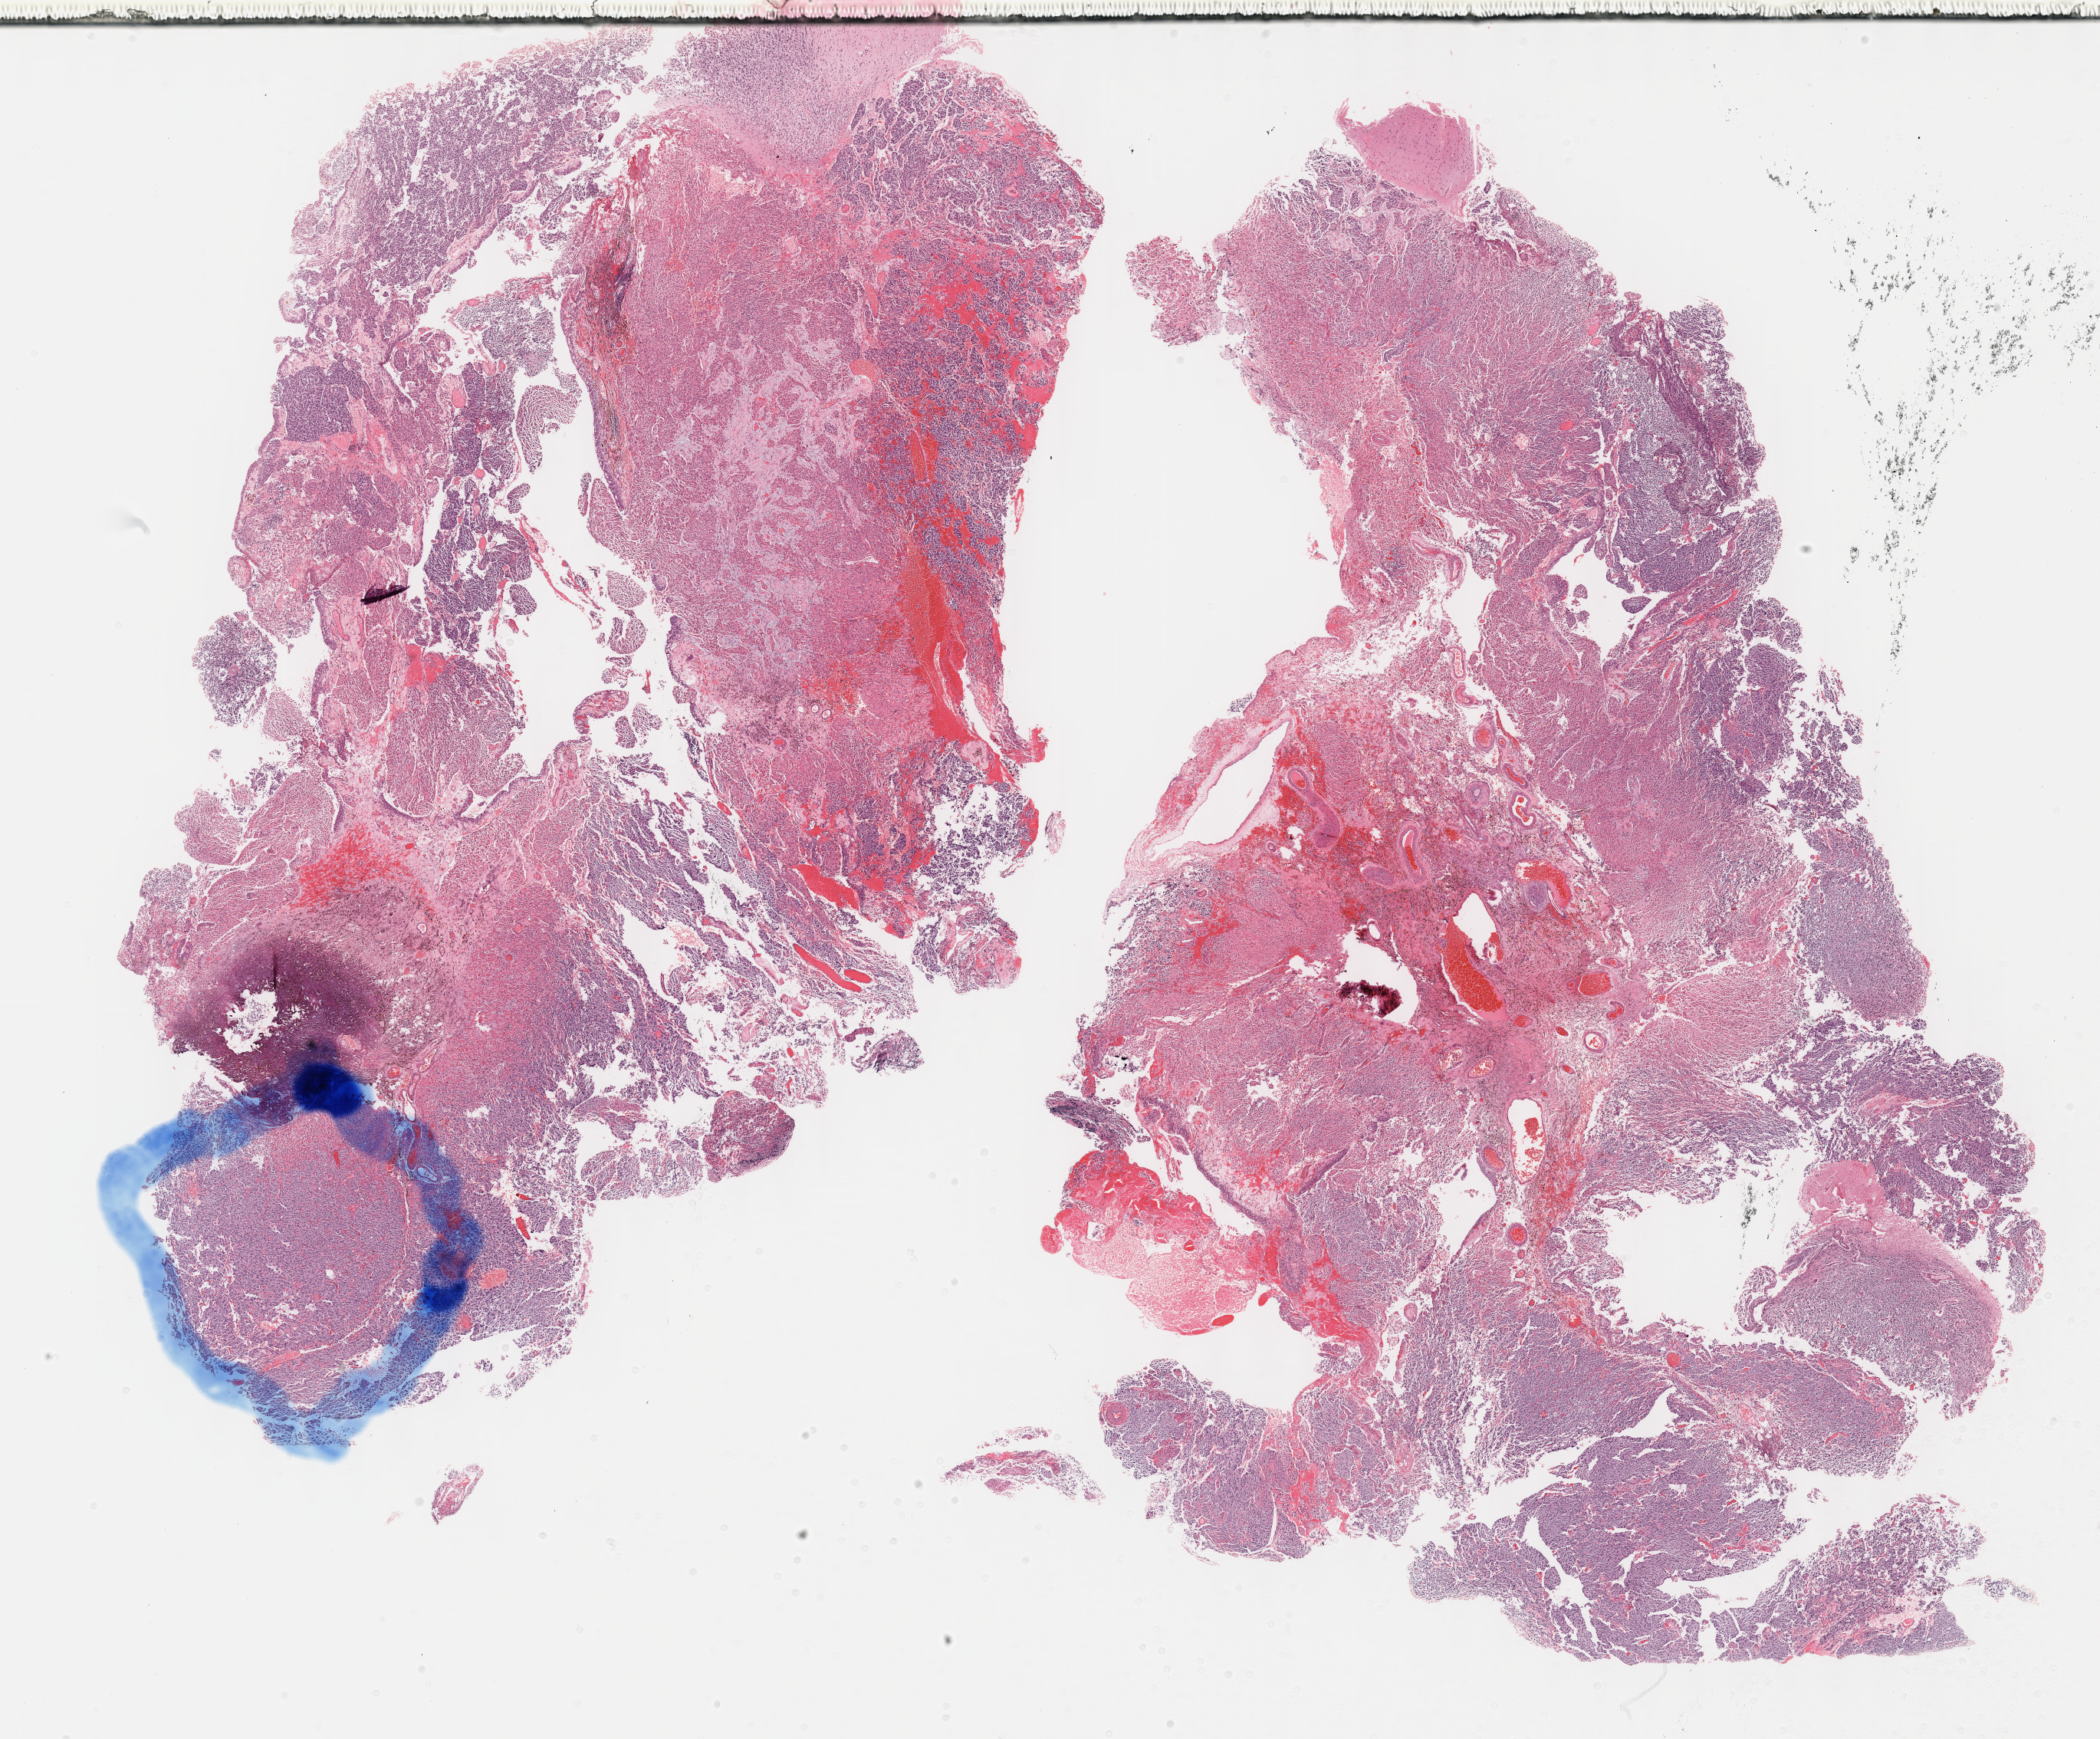
H&E-stained whole-slide image — a low-resolution overview of the entire scanned area, about 22.1 x 18.3 mm, formalin-fixed paraffin-embedded (FFPE) diagnostic section, sample: primary tumour, brain. Male patient; age at initial diagnosis 66 years.
- pathologic diagnosis: Glioblastoma